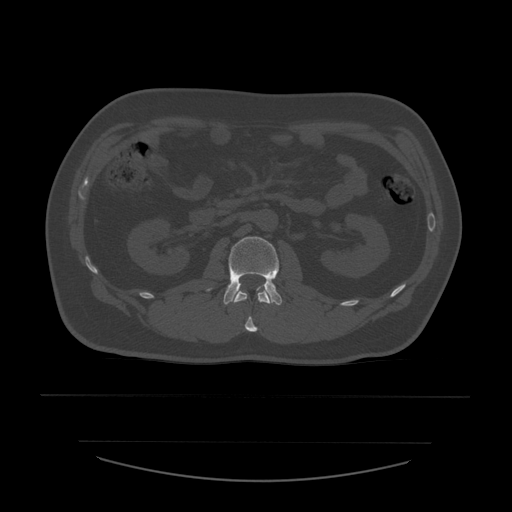
CT including the spine, one axial slice; slice 209 of 532 in the series (ordered by position); reconstruction kernel STANDARD; bone window (W 1800 / L 400 HU); 512 × 512 image matrix, field of view 441 × 441 mm. Patient age 44 years. From the clinical record (not read from this slice): primary cancer: soft tissue sarcoma.
Annotated regions visible in this slice (semi-automatic segmentation, software-assisted and operator-edited):
- L1 vertebra: bounding box <232,289,273,332> (left, top, right, bottom; pixels)
- L2 vertebra: <207,237,283,306>